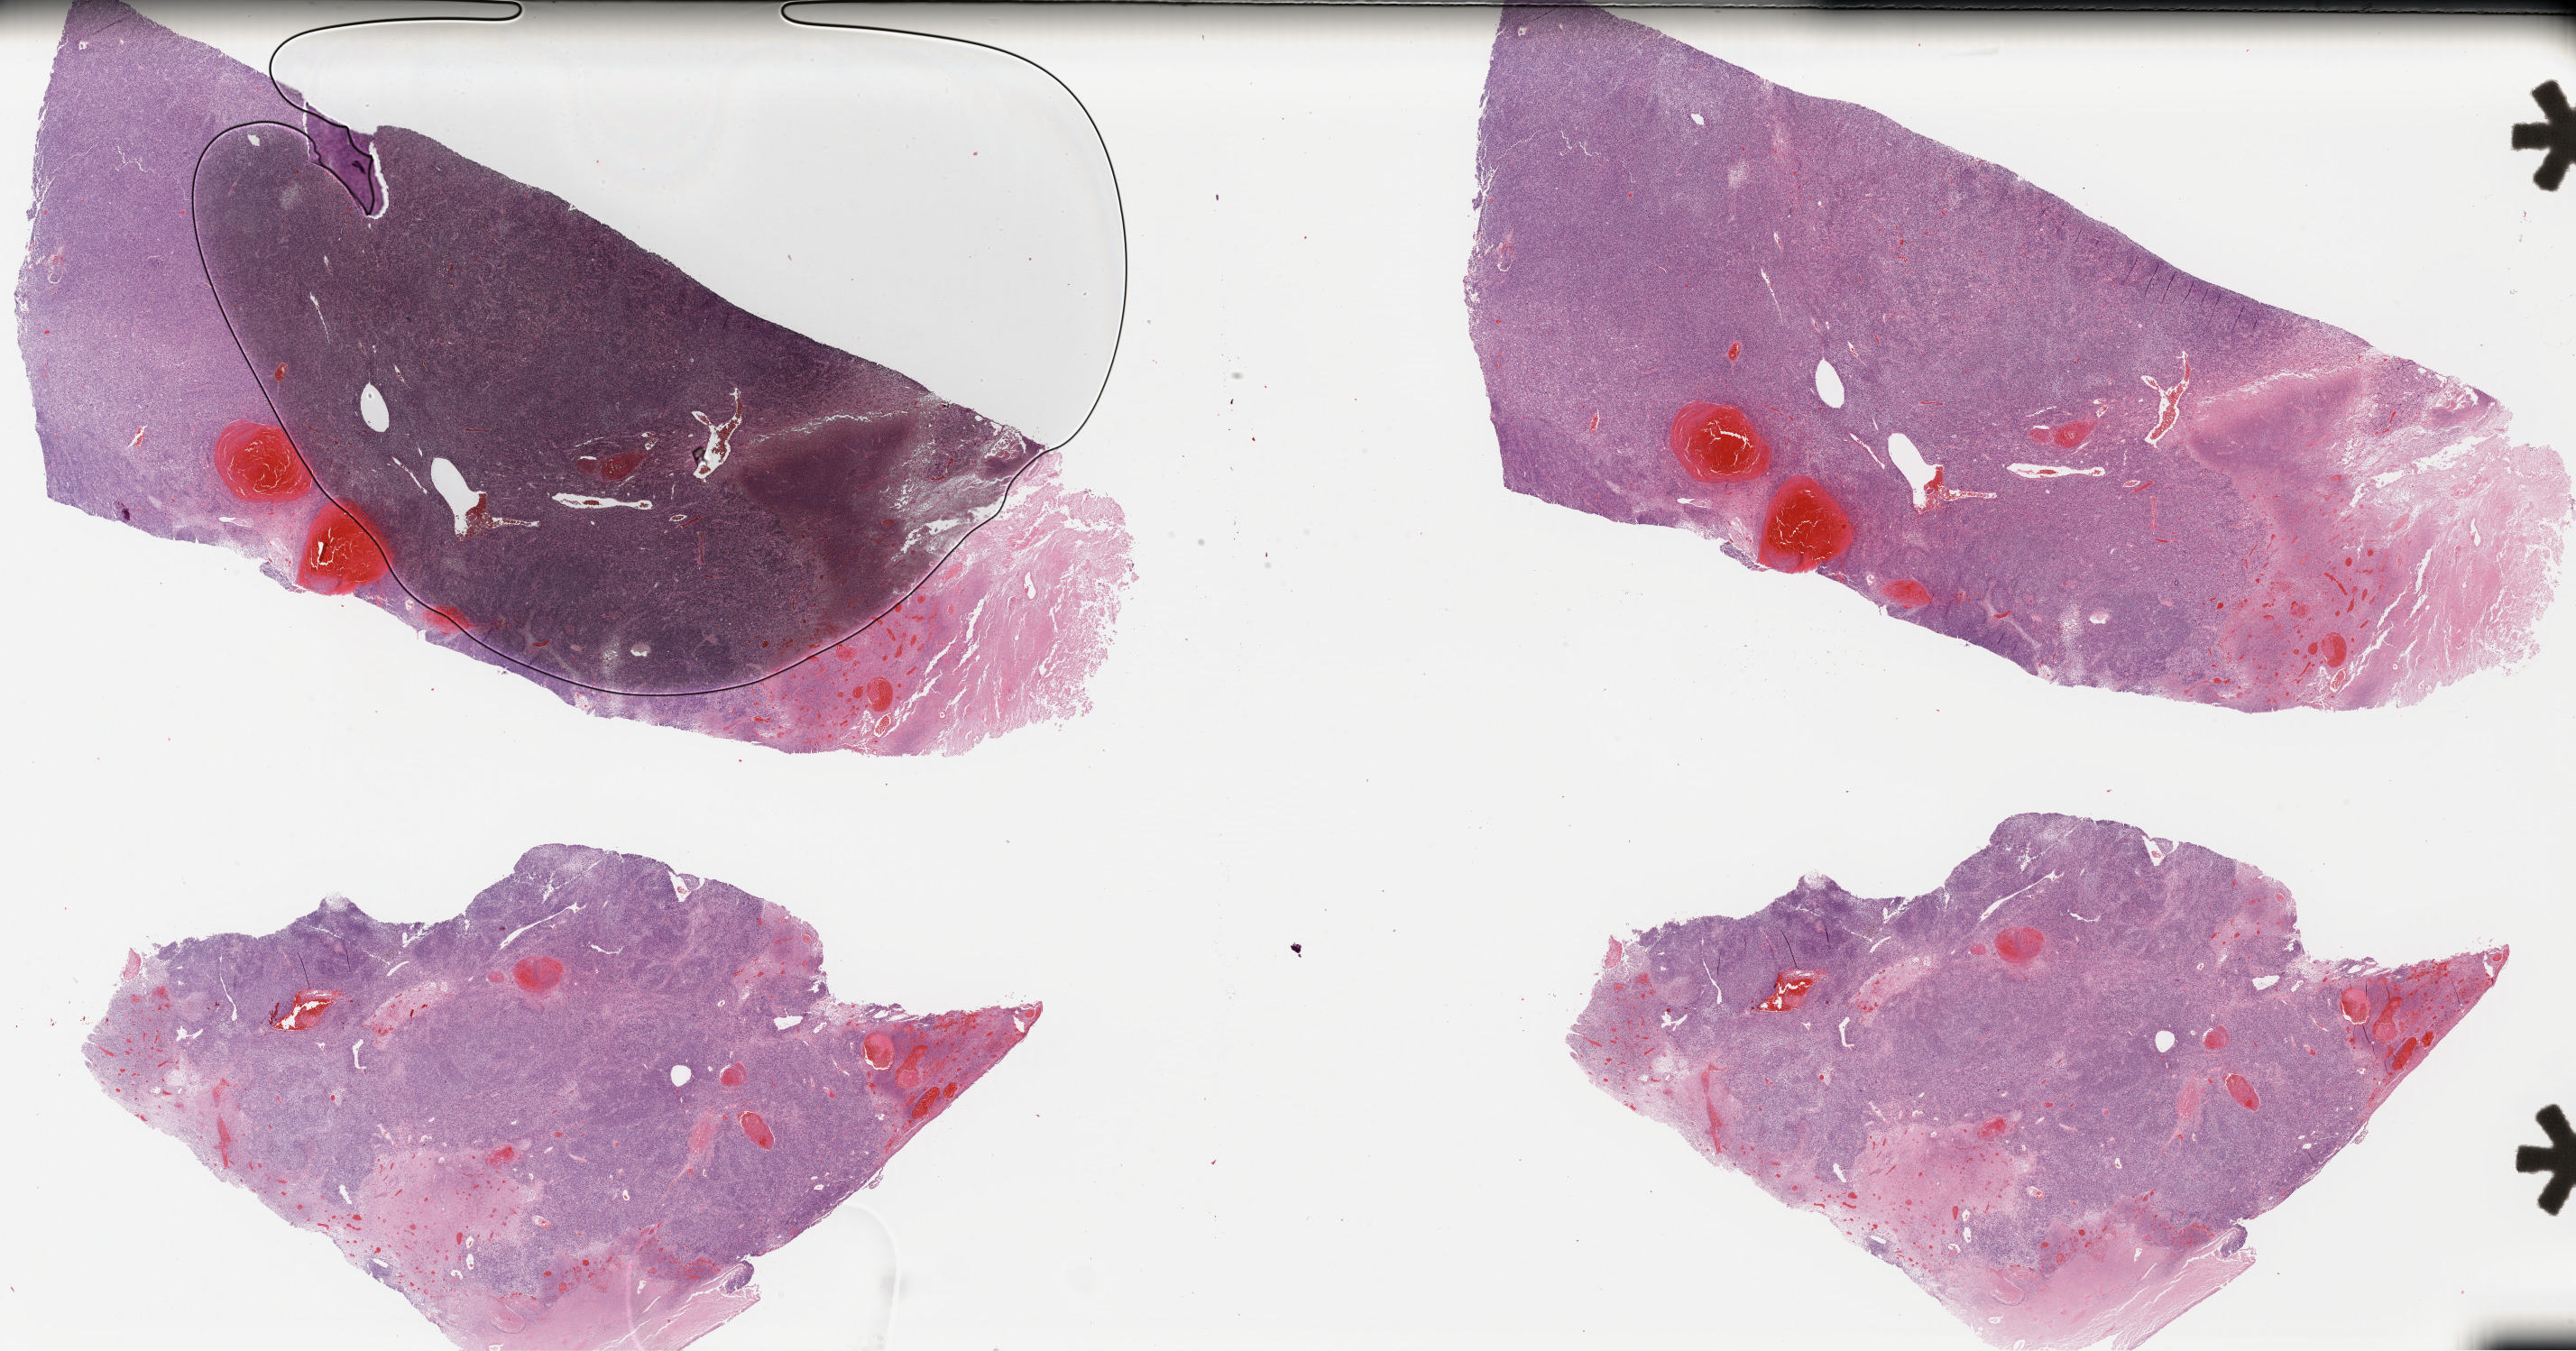
Digitized H&E-stained tissue section (whole slide), a low-resolution overview of the entire scanned area, about 44.9 x 23.5 mm, FFPE section, uterus, primary tumour sample. Female patient; age at initial diagnosis 63 years.
Diagnosis: Mullerian mixed tumor (endometrium).